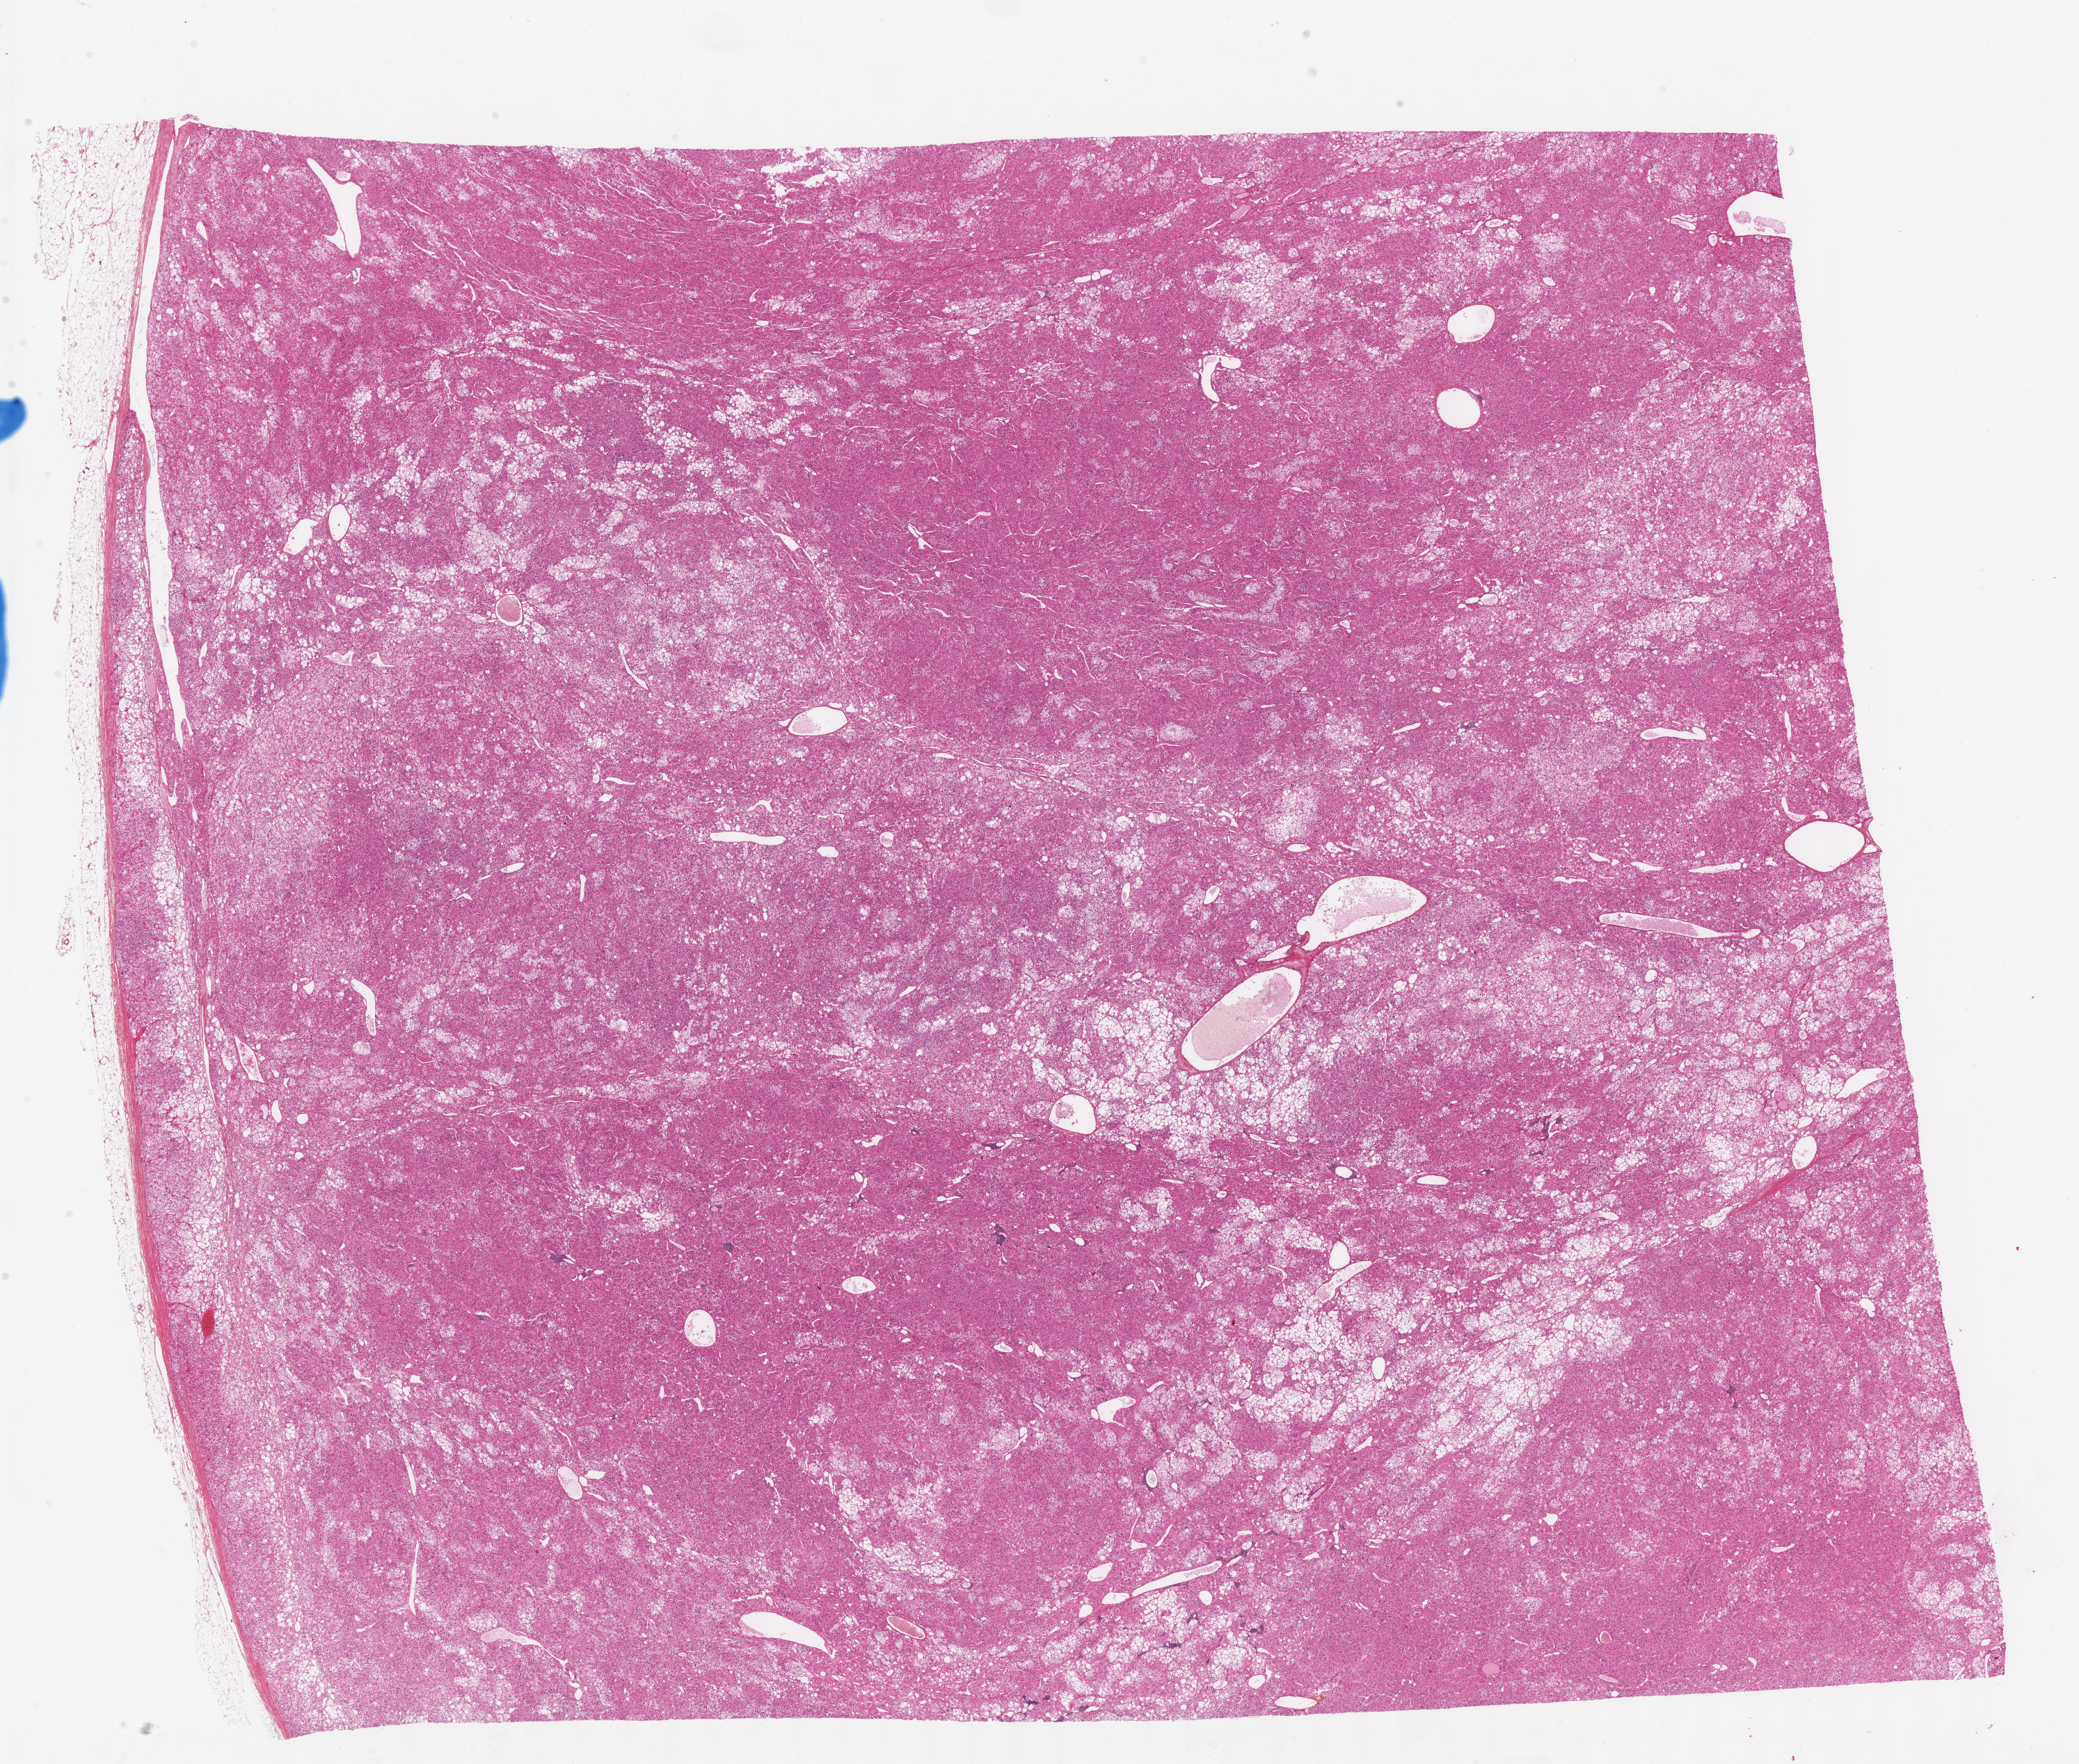
Whole-slide histology image, Hematoxylin and eosin (H&E) stained — a low-resolution overview of the entire scanned area, about 24.1 x 20.5 mm (slide scanned at 40x), formalin-fixed paraffin-embedded (FFPE) diagnostic section, primary tumour sample from the adrenal cortex. Patient: female, age at initial diagnosis 75 years.
Diagnosis: Adrenal cortical carcinoma.